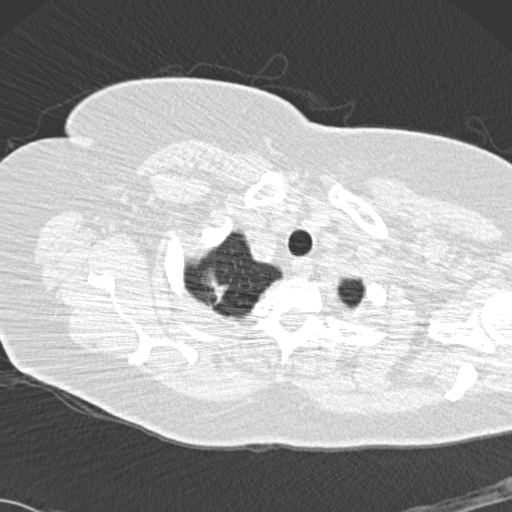
Low-dose screening chest CT, one axial slice; slice 133 of 146 in the series (ordered by position); 120 kVp; lung window (W 1500 / L -600 HU); 2 mm slice thickness; 512 × 512 image matrix, field of view 350 × 350 mm.
Annotated regions visible in this slice (manually delineated by an expert):
- lesion 1 (tumor, upper lobe of right lung): box from (x=207, y=273) to (x=228, y=303) px